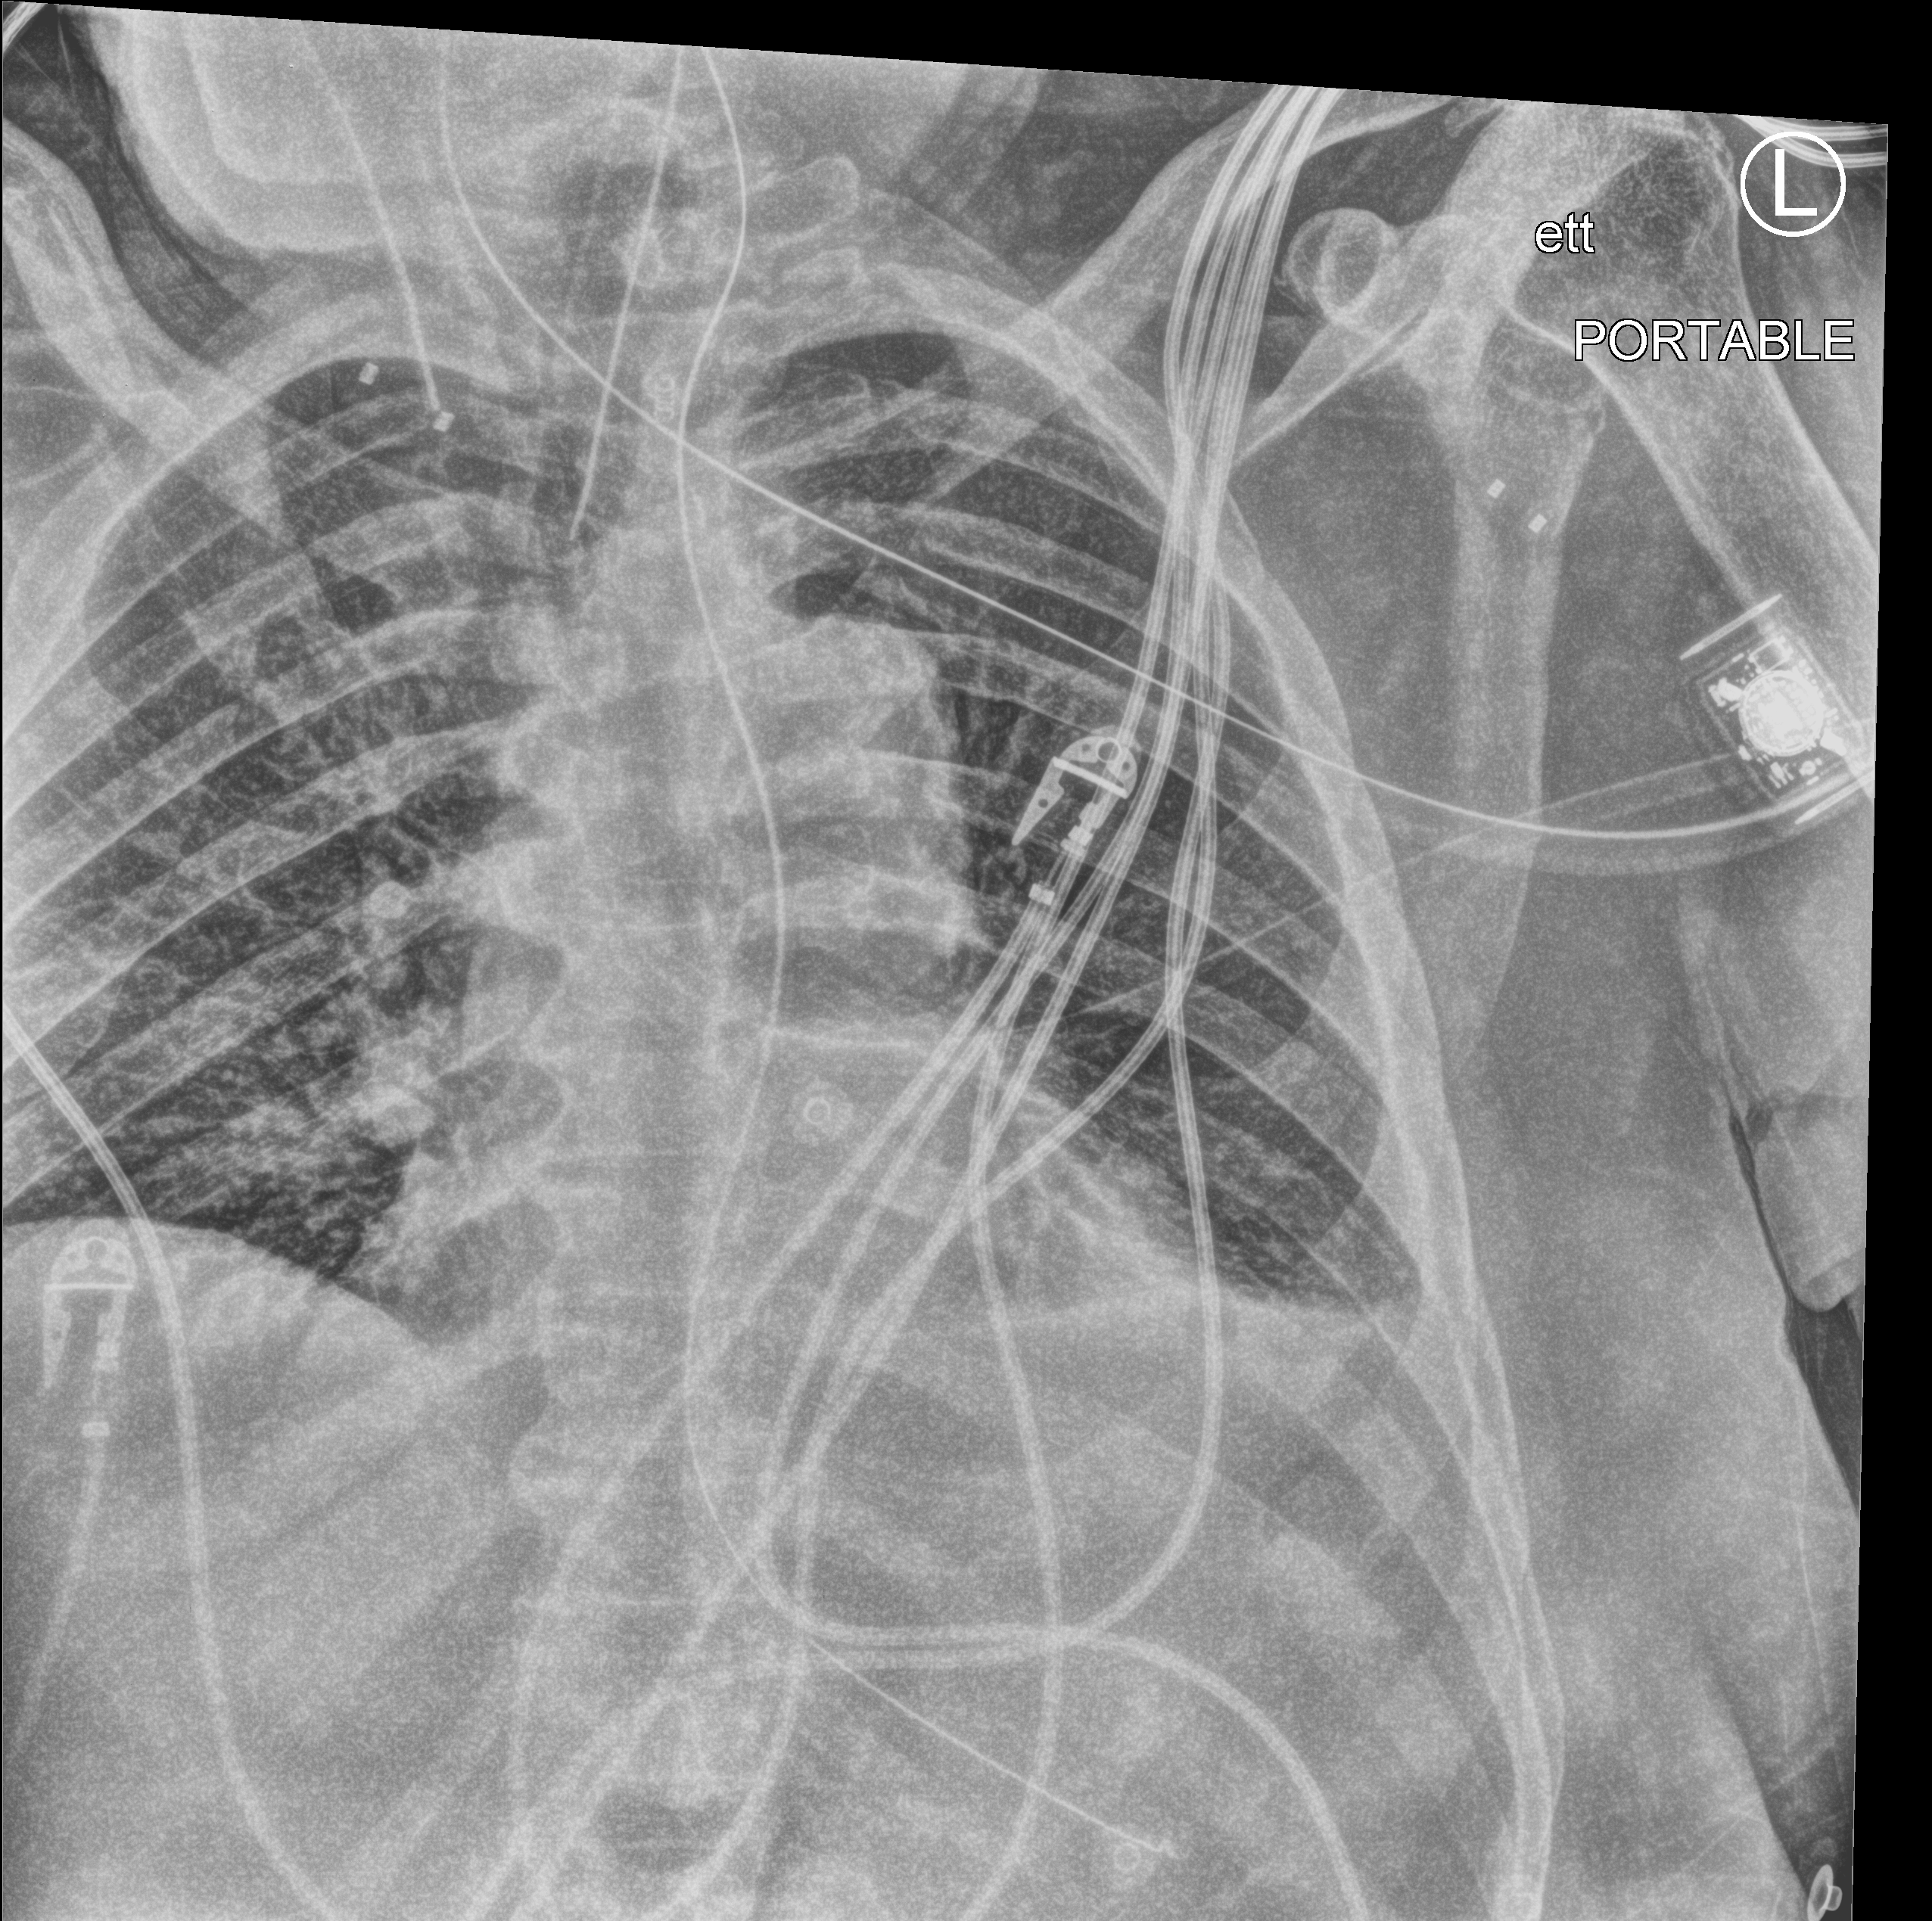
Portable chest radiograph; anteroposterior (AP) projection. Male patient hospitalised with COVID-19, age 75–90 years.
Hospital-stay facts (about this admission, not read from this image; timing relative to this image not recorded):
- length of hospital stay: 12 days
- mechanically ventilated during this hospital stay: yes
- admitted to intensive care during this hospital stay: yes